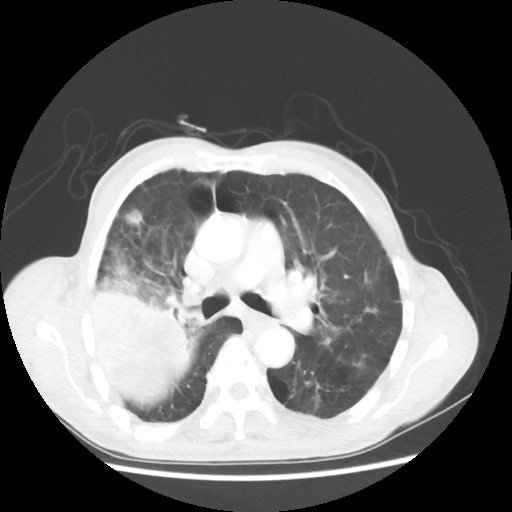
Chest CT, one axial slice. Position 34 of 58 along the scan axis. 100 kVp. Lung window (W 1500 / L -600 HU). 512 × 512 image matrix, field of view 351 × 351 mm. Patient: male, 75 years. Case-level facts recorded for this patient, not image findings: clinical TNM (as recorded): T4 N1 M1.
Structures marked on this image (rectangle marked by the reading radiologist):
- lung tumour (recorded histology: adenocarcinoma): box from (x=77, y=261) to (x=195, y=409) px